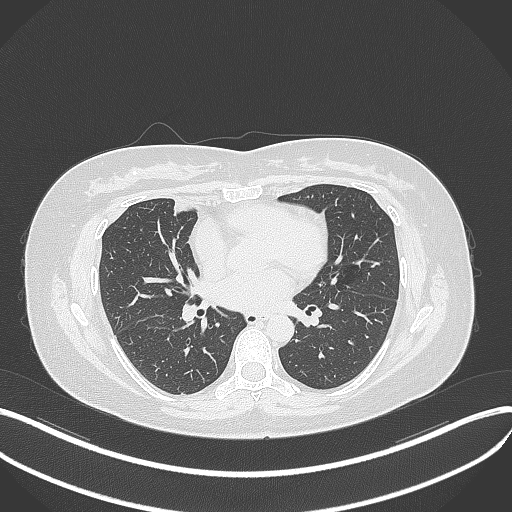
Chest CT, one axial slice; slice 150 of 273 in the series (ordered by position); reconstruction kernel B70f; lung window (W 1500 / L -600 HU); 1 mm slice thickness; 512 × 512 image matrix, field of view 400 × 400 mm. Female patient, age 42 years. From the clinical record (not read from this slice): clinical TNM (as recorded): T1b N0 M0.
Structures marked on this image (rectangle marked by the reading radiologist):
- lung tumour (recorded histology: adenocarcinoma): bounding box (x1, y1, x2, y2) in pixels: (169, 193, 195, 219)